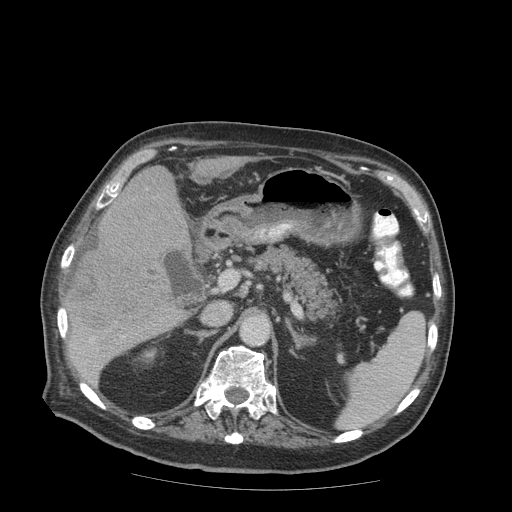
Contrast-enhanced abdominal CT (liver protocol), one axial slice. Slice 45 of 99 in the series (ordered by position). Soft-tissue window (W 400 / L 40 HU). 2.5 mm slice thickness. 512 × 512 image matrix. From the clinical record (not read from this slice): diagnosis: hepatocellular carcinoma (patient treated with transarterial chemoembolisation; whether this scan precedes or follows treatment is not stated here); TNM stage (as recorded): Stage-IIIB; Child-Pugh class: A; tumour differentiation: well differentiated; tumour nodularity: multinodular.
Structures marked on this image (semi-automatically segmented with operator editing):
- liver parenchyma outside the tumour (the mass and vessels are separate outlines, so this box may not span the whole liver): box from (x=66, y=161) to (x=199, y=384) px
- mass: (x=64, y=190)–(x=184, y=330)